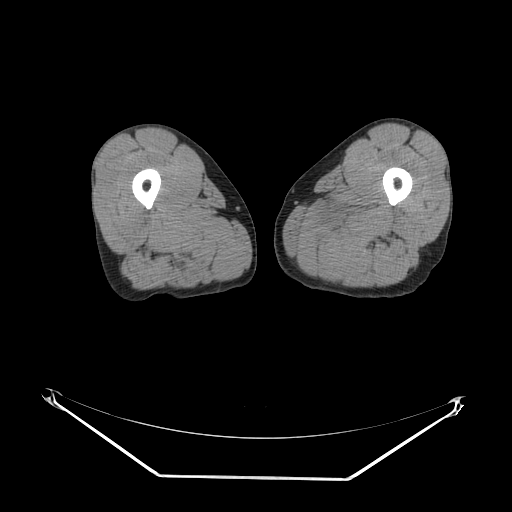
CT of an extremity soft-tissue mass (from a PET/CT study), one axial slice. Position 11 of 267 along the scan axis. Reconstruction kernel SOFT. Soft-tissue window (W 400 / L 40 HU). 512 × 512 image matrix, field of view 500 × 500 mm. Male patient. From the clinical record (not read from this slice): histological type: pleiomorphic liposarcoma; grade: high; site of the primary tumour: left thigh.
Outlined on this slice (expert contour drawn on MRI and transferred to this co-registered scan by the dataset authors):
- gross tumour volume including surrounding oedema: bounding box <322,201,371,250> (left, top, right, bottom; pixels)